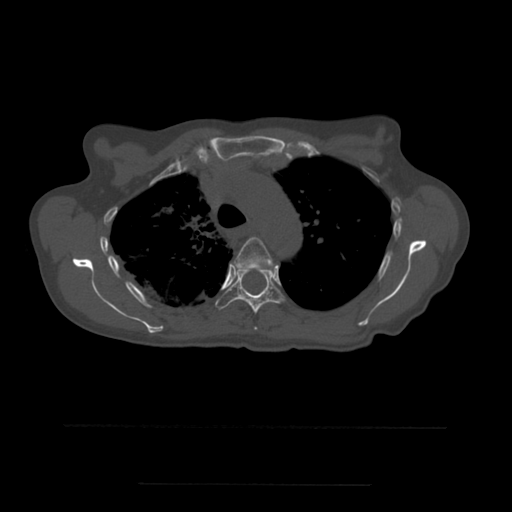
CT including the spine, one axial slice. Position 397 of 544 along the scan axis. Bone window (W 1800 / L 400 HU). 1.25 mm slice thickness. 512 × 512 image matrix, field of view 350 × 350 mm. Patient age 58 years. Case-level facts recorded for this patient, not image findings: primary cancer: lung.
Structures marked on this image (semi-automatically segmented with operator editing):
- T4 vertebra: bounding box <234,237,274,330> (left, top, right, bottom; pixels)
- T5 vertebra: <215,263,284,314>